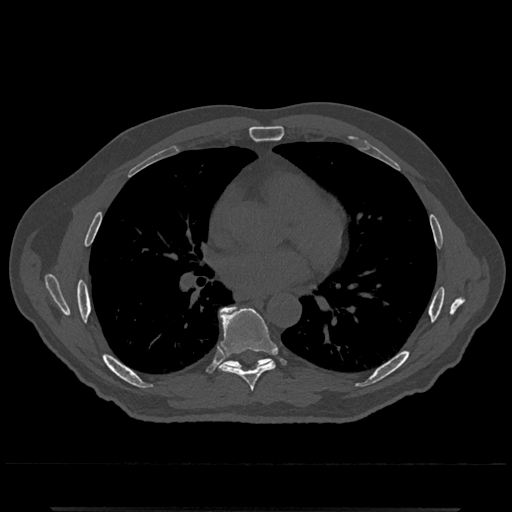
CT including the spine, one axial slice. Slice 707 of 797 in the series (ordered by position). Reconstruction kernel Br40s/3. 120 kVp. Bone window (W 1800 / L 400 HU). 0.5 mm slice thickness. 512 × 512 image matrix. Male patient, age 67 years. From the clinical record (not read from this slice): primary cancer: prostate.
Annotated regions visible in this slice (semi-automatic segmentation, software-assisted and operator-edited):
- T7 vertebra: bounding box [x1, y1, x2, y2] px = [219, 308, 276, 391]
- T8 vertebra: [219, 306, 271, 369]